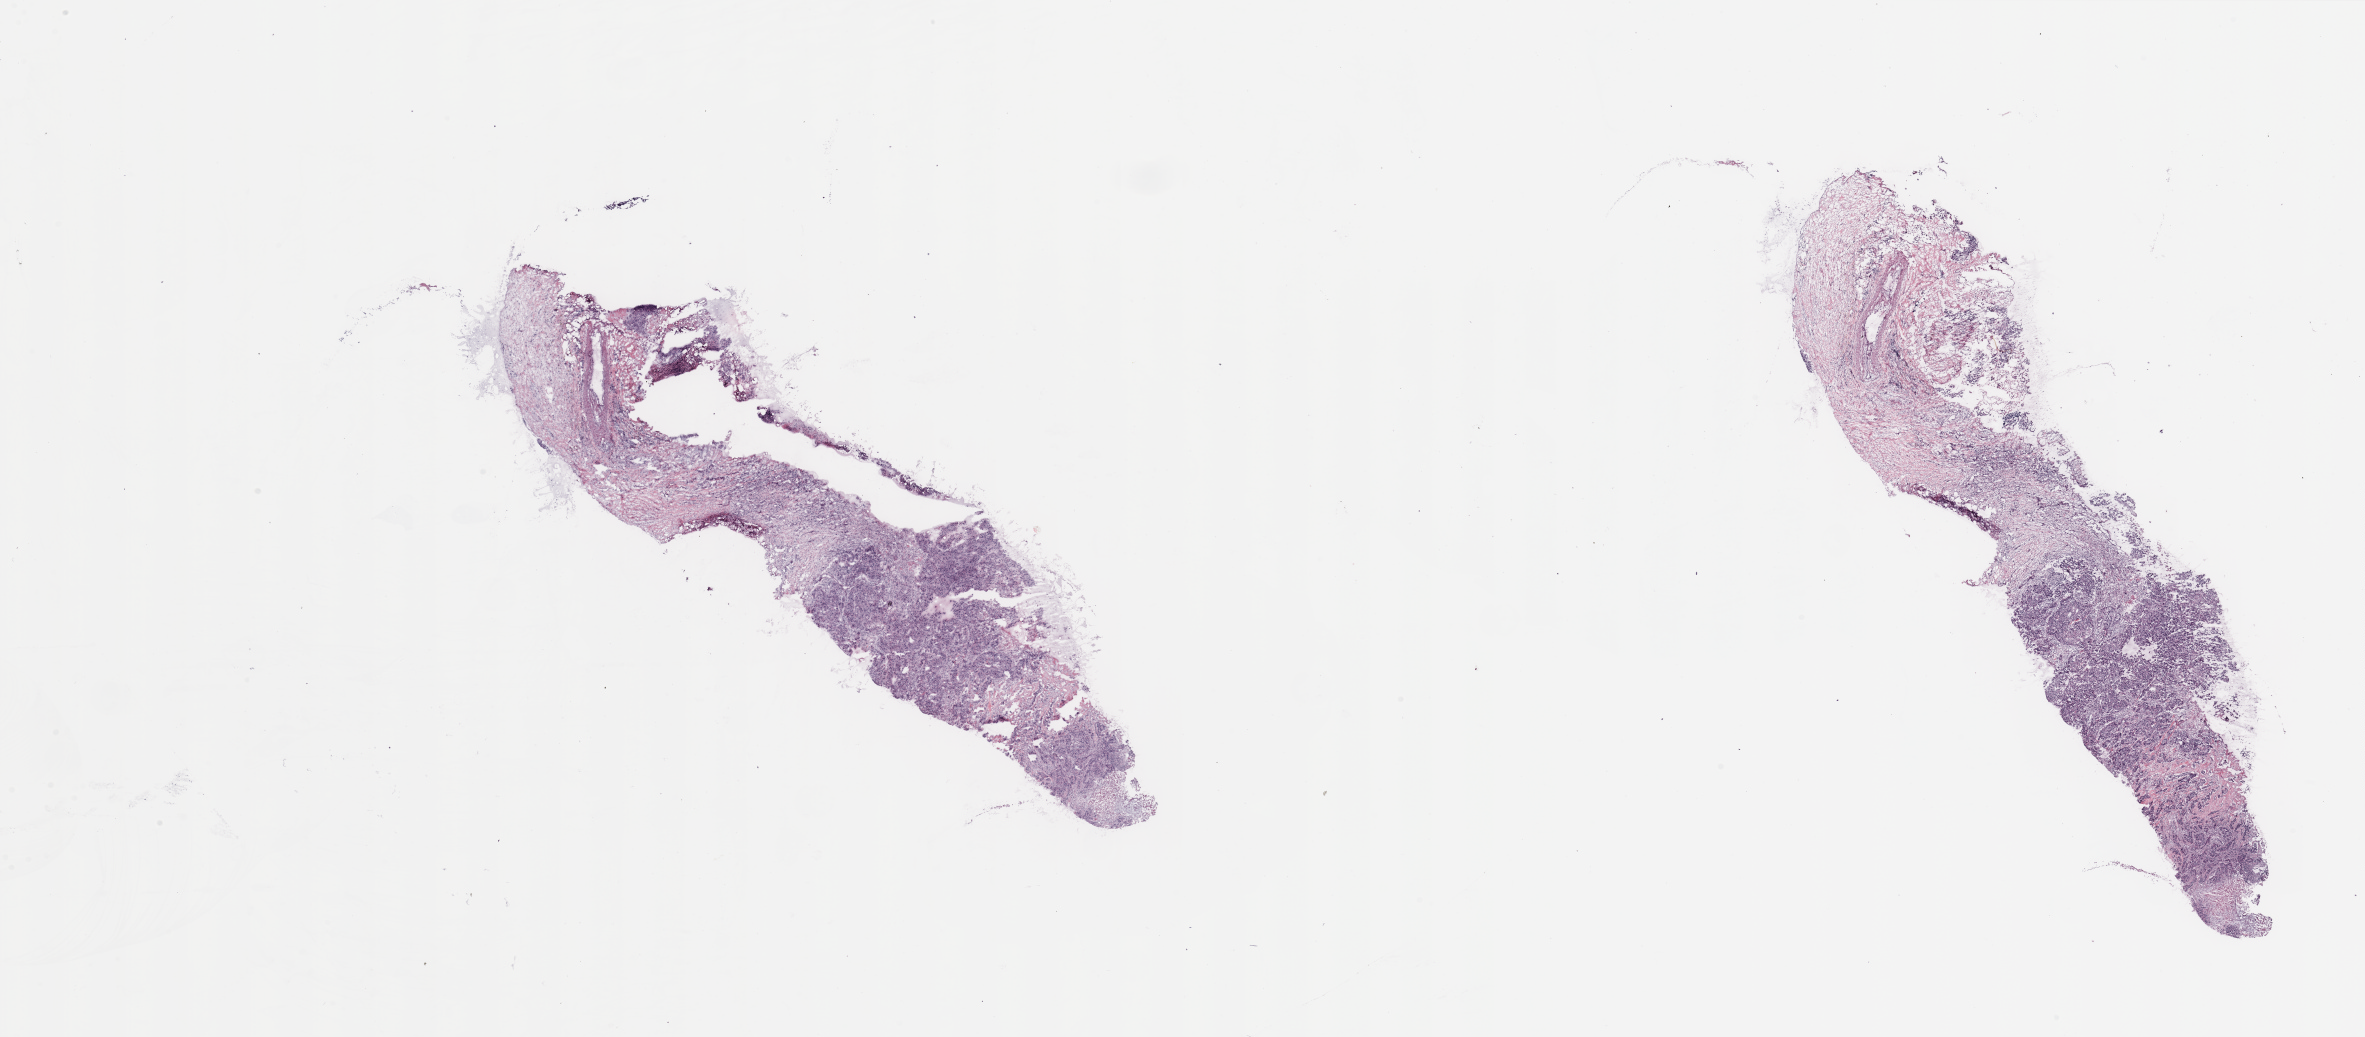
Digitized H&E-stained tissue section (whole slide), low-resolution overview of the scanned area, about 37.4 x 16.4 mm. Breast, tumour tissue. 55-year-old female patient.
Histologic diagnosis: Infiltrating duct carcinoma, NOS. AJCC pathologic stage: IIB.